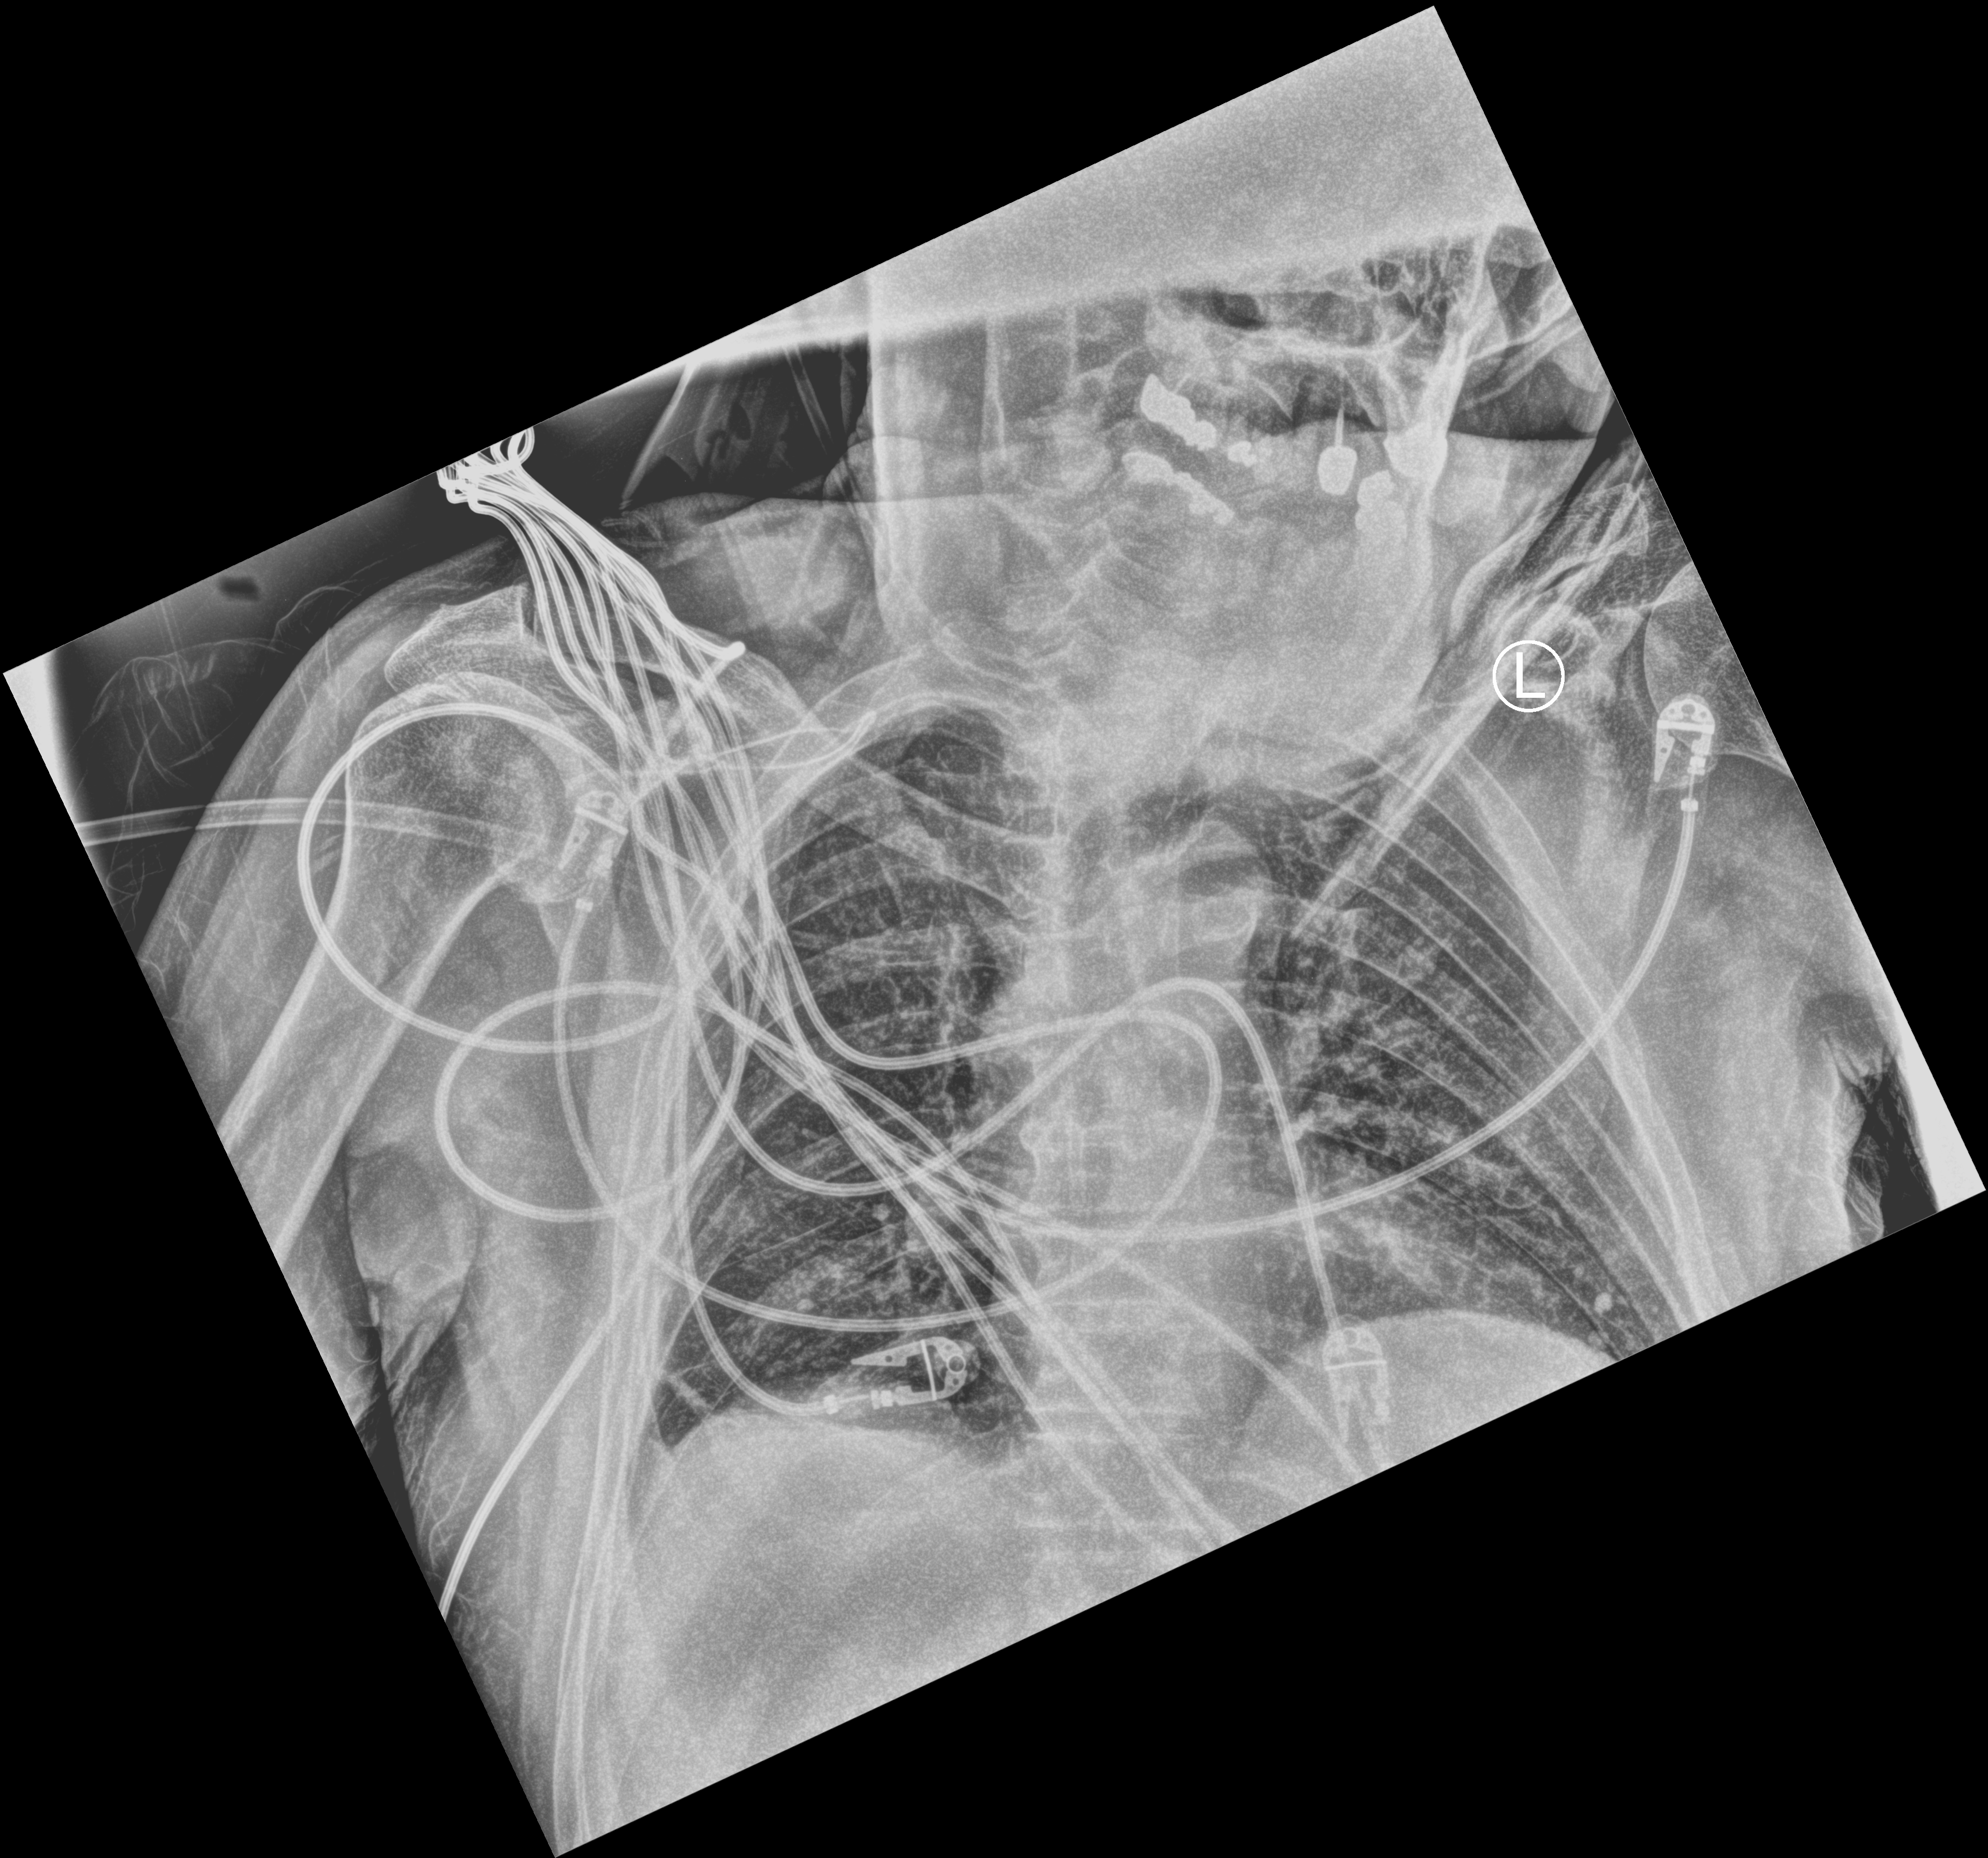
Bedside chest radiograph (computed radiography), anteroposterior (AP) projection. Patient hospitalised with COVID-19; male, aged 75–90 years.
Hospital-stay facts (about this admission, not read from this image; timing relative to this image not recorded): admitted to intensive care during this hospital stay: no; mechanically ventilated during this hospital stay: no; other chronic lung disease (admission record): no.